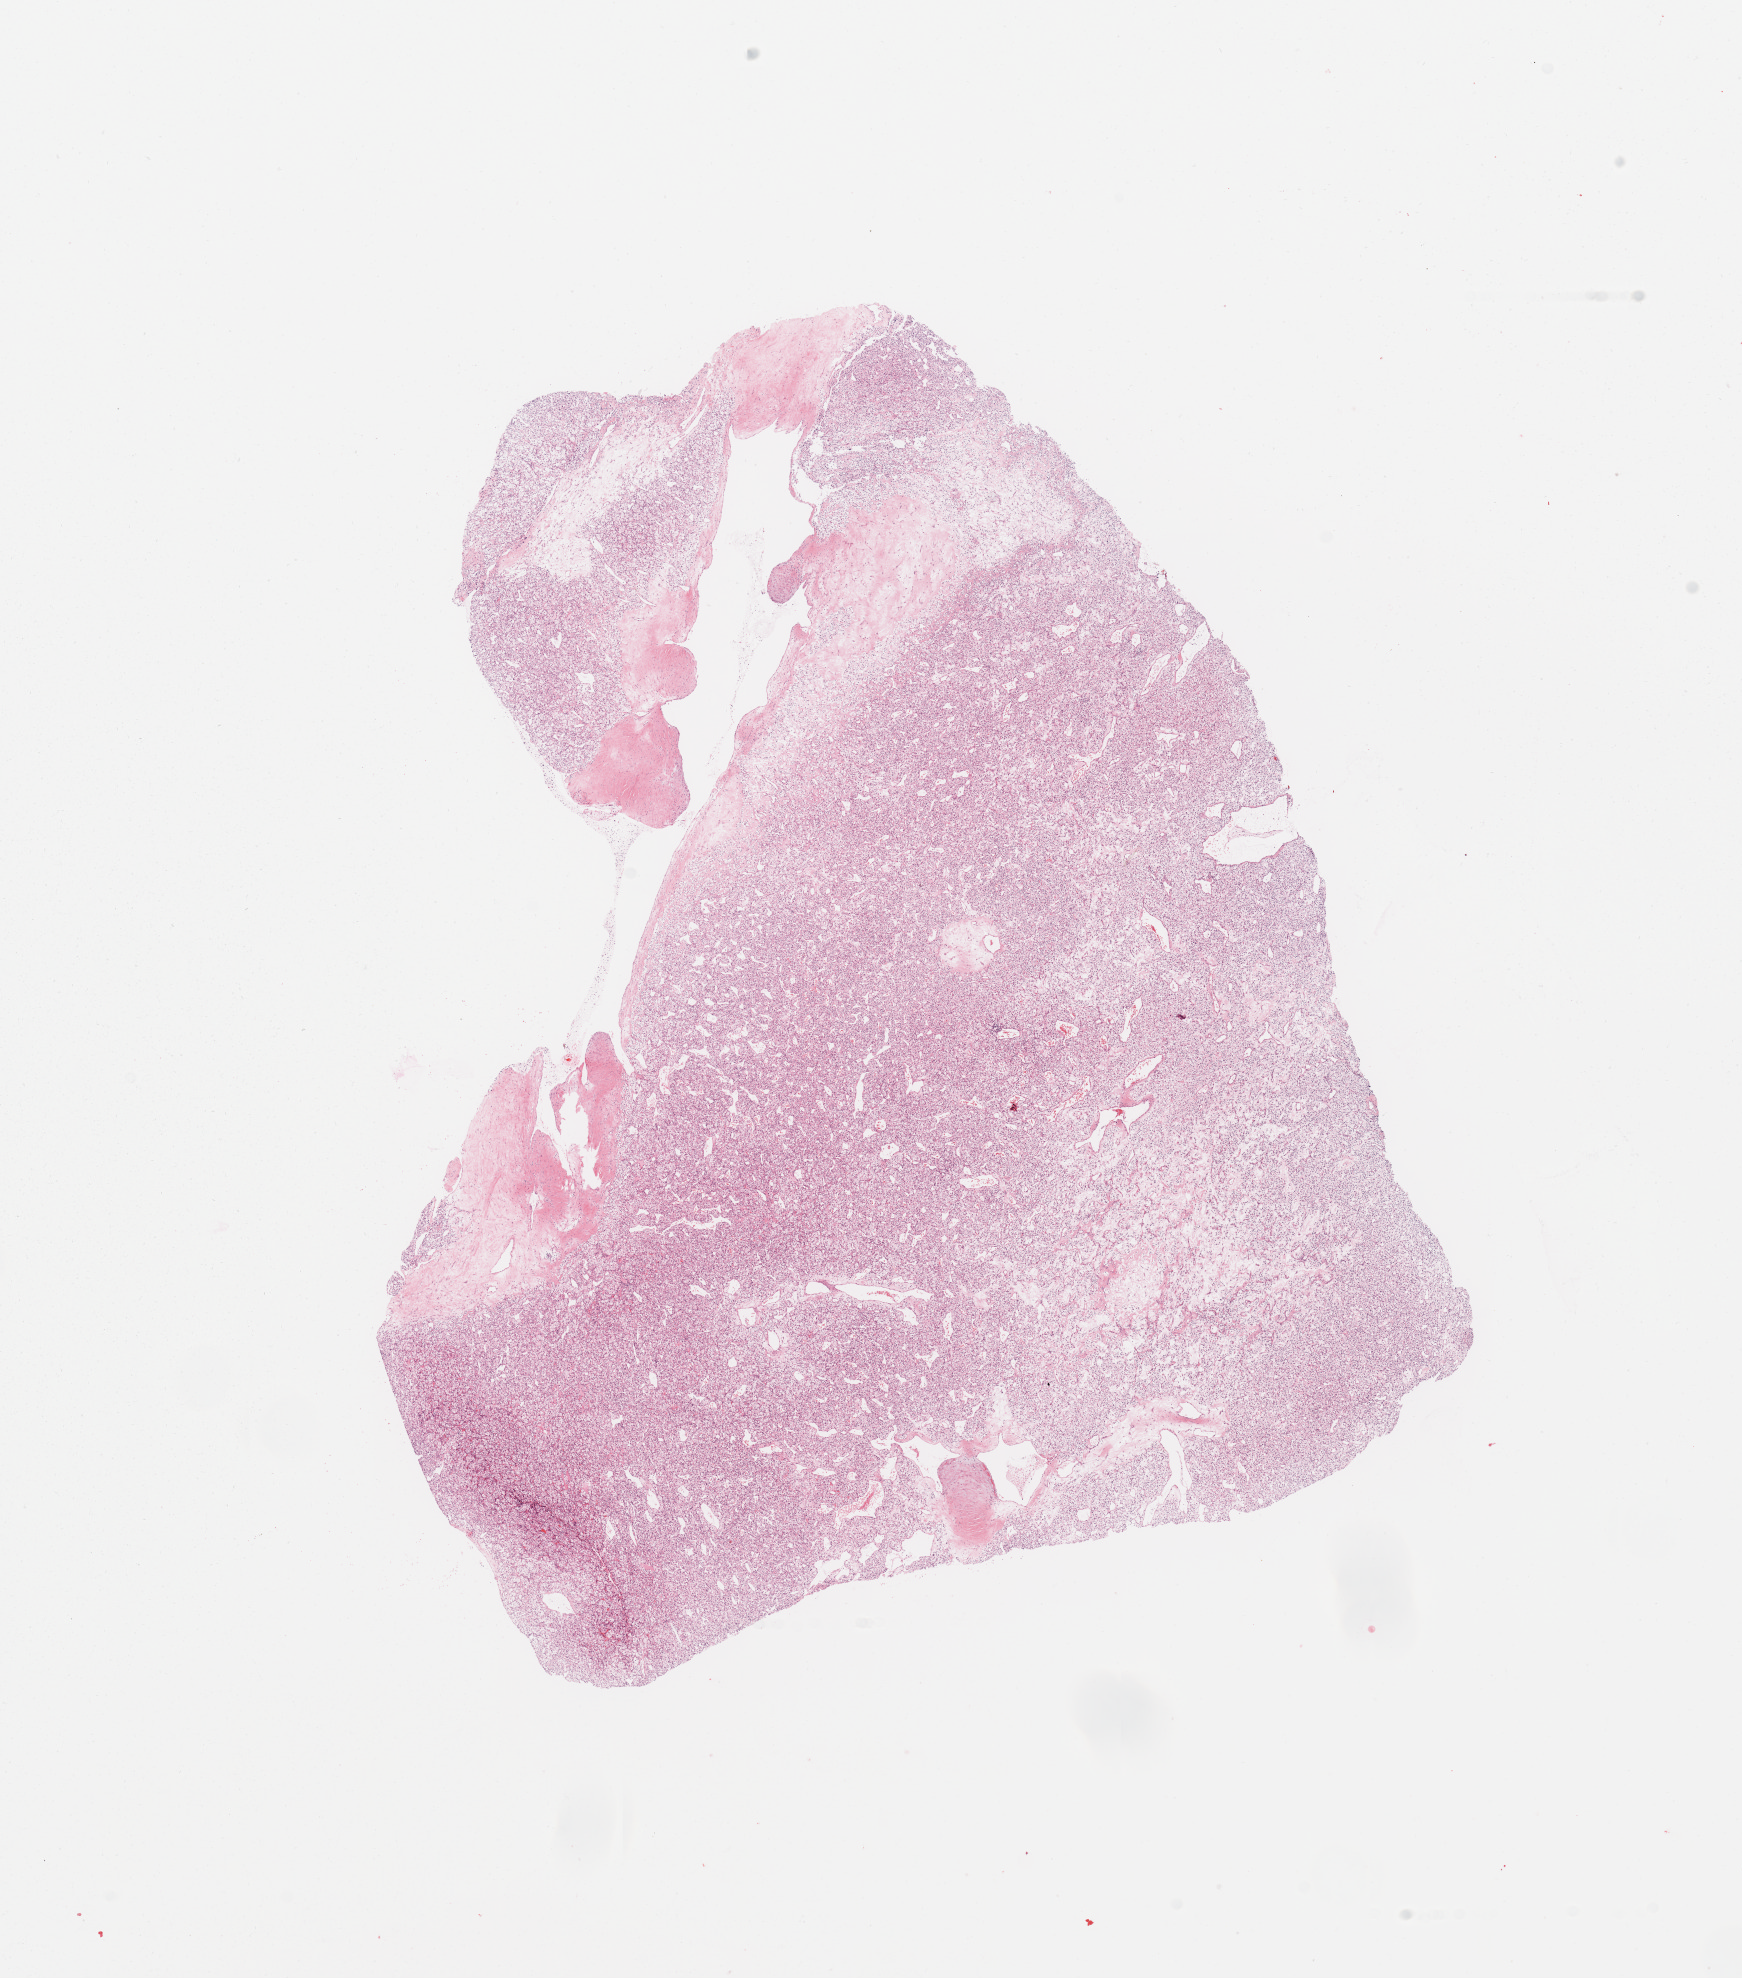
Digitized H&E tissue section (whole slide) — a low-resolution overview of the entire scanned area, about 13.8 x 15.6 mm; tumour tissue sample, sampled site: kidney. 47-year-old male patient. Histologic grade: G2 (moderately differentiated). Pathologist review of this section (percent, as recorded): tumour nuclei 80%, necrosis 3%.
AJCC pathologic stage: IV. Diagnosis: Renal cell carcinoma, NOS.